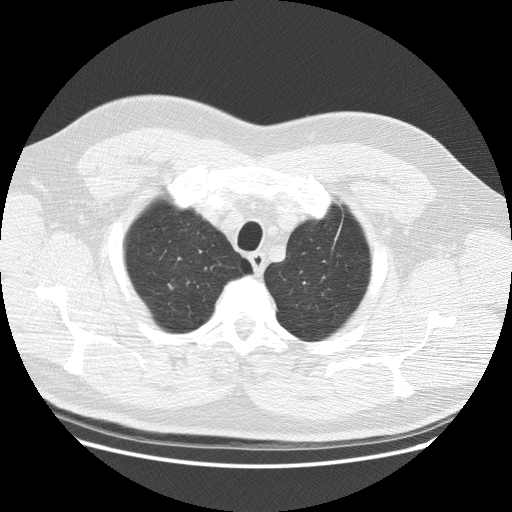
Low-dose screening chest CT, one axial slice. Slice 96 of 111 in the series (ordered by position). Lung window (W 1500 / L -600 HU). 2.5 mm slice thickness. 512 × 512 image matrix, field of view 389 × 389 mm.
Structures marked on this image (expert manual segmentation):
- lesion 1 (tumor, upper lobe of right lung): bounding box [x1, y1, x2, y2] px = [168, 284, 173, 289]